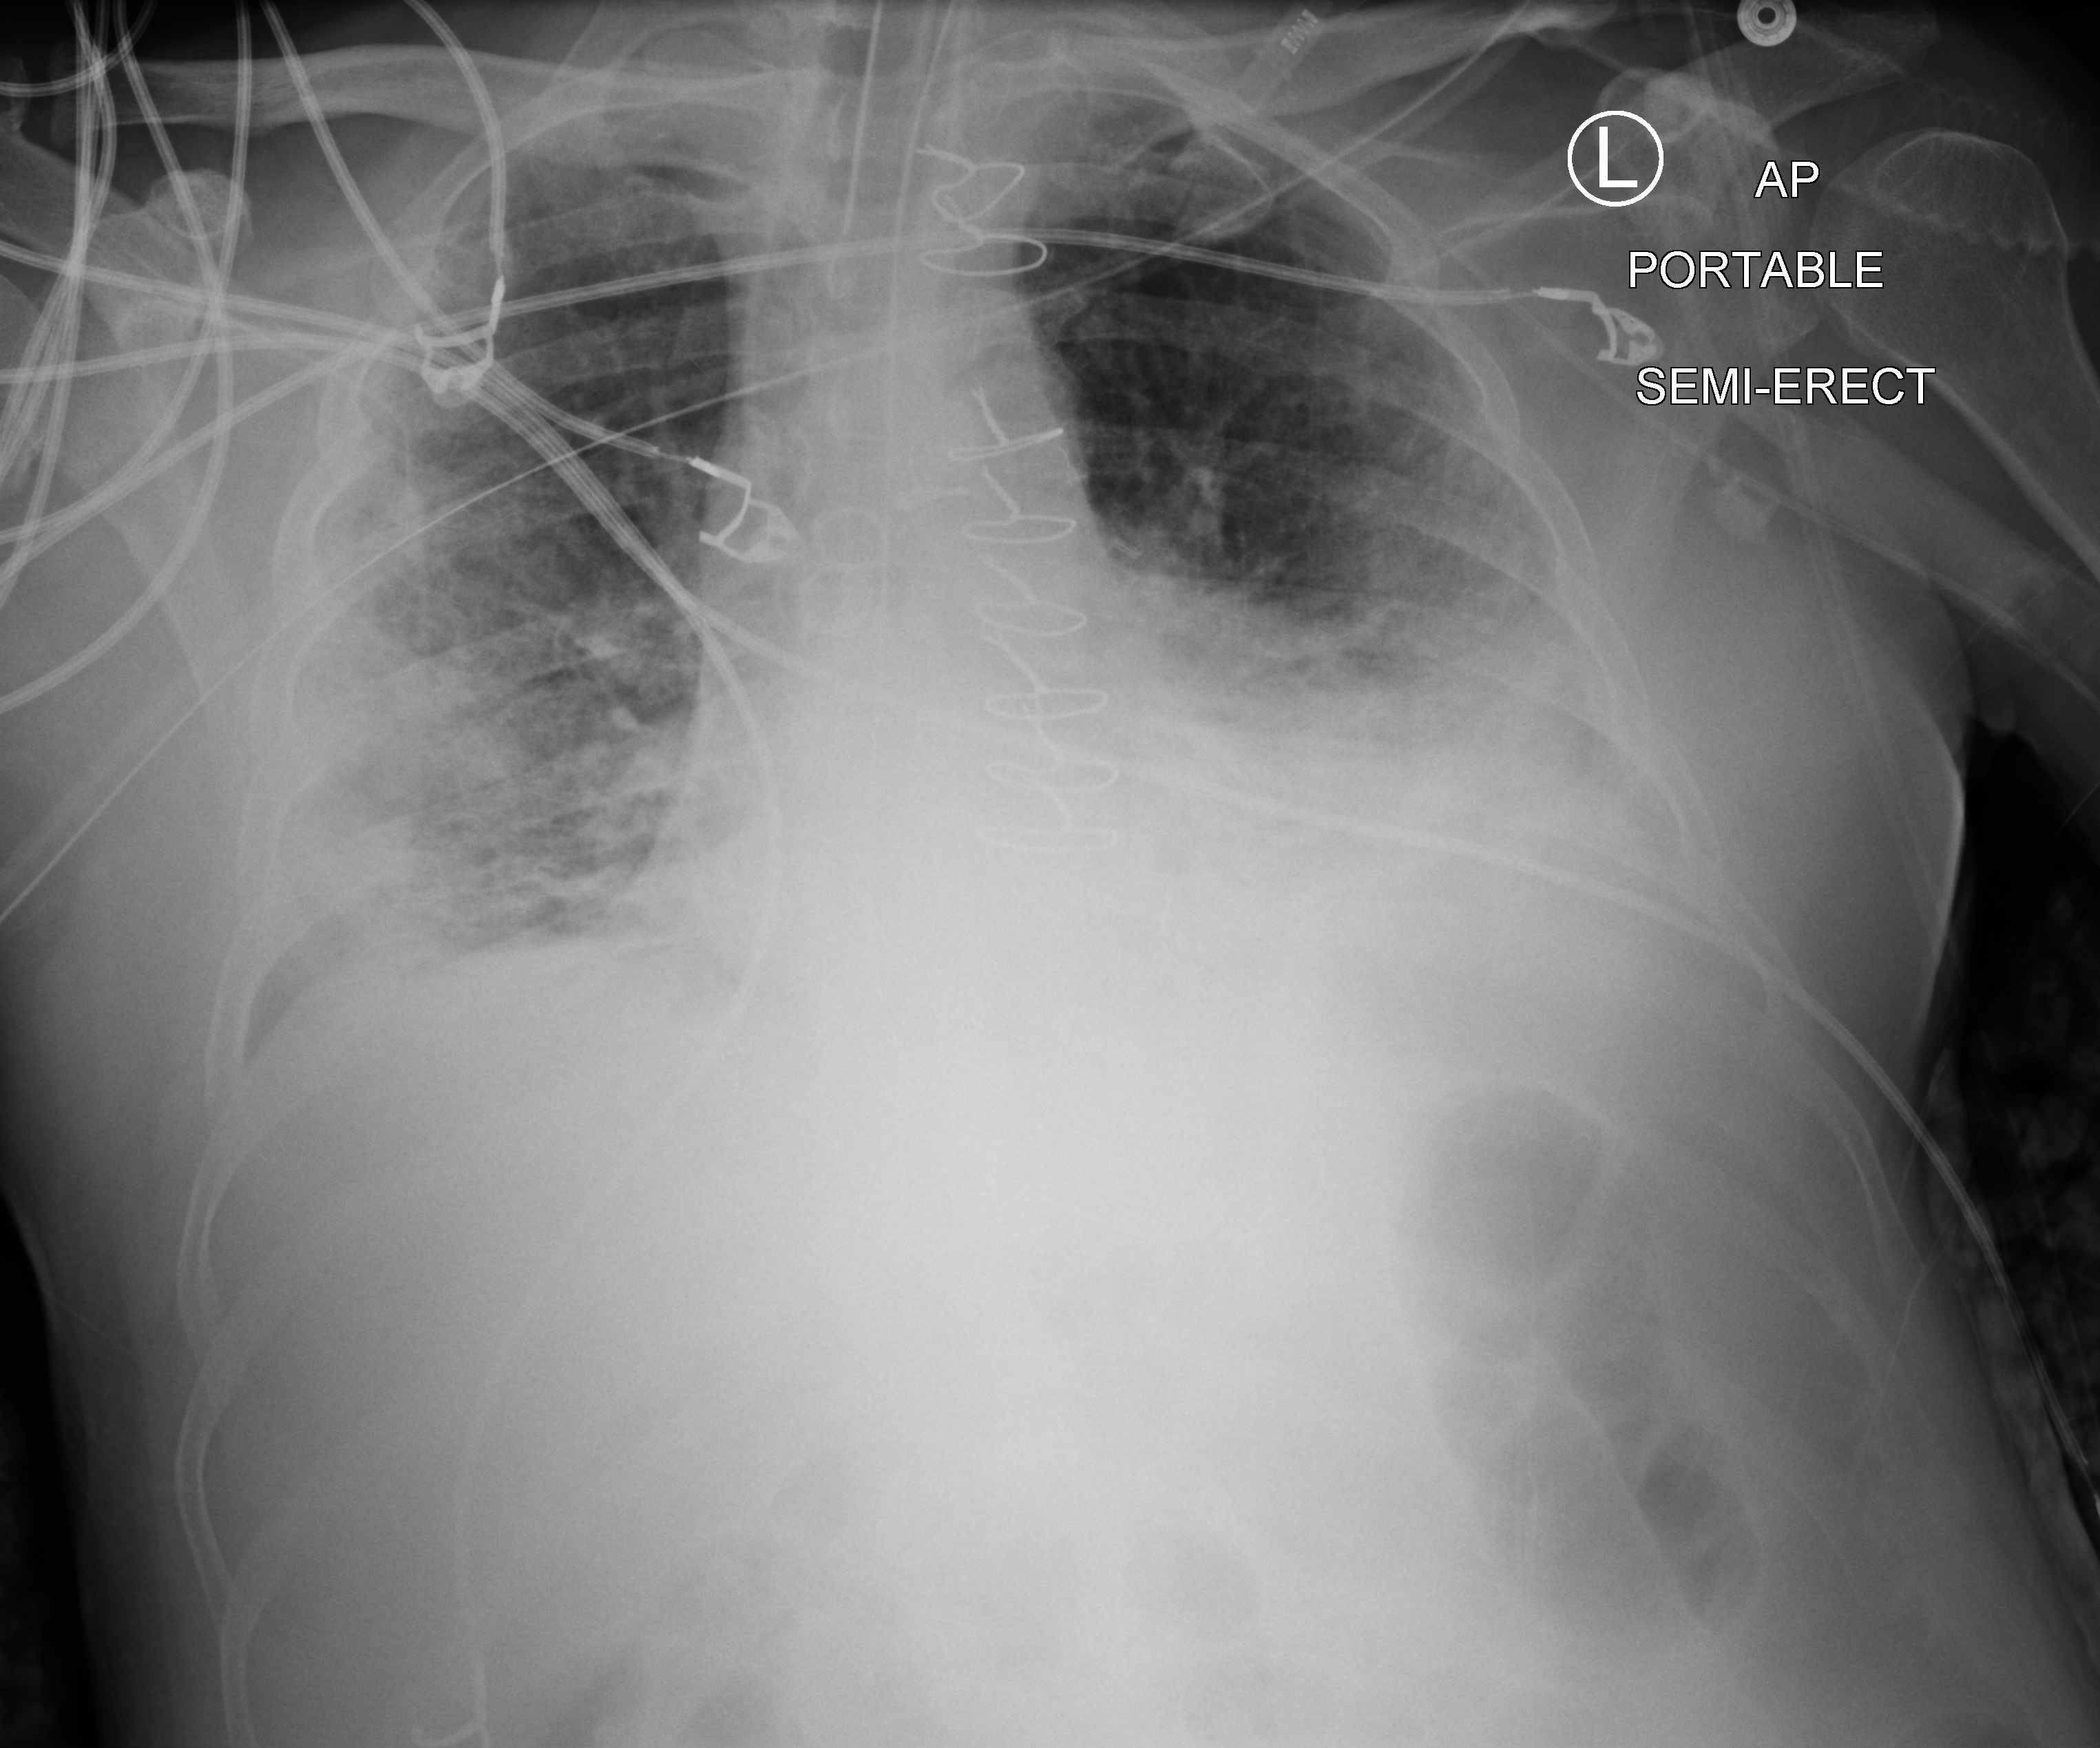
Portable chest radiograph, anteroposterior (AP) projection. Patient hospitalised with COVID-19; male, aged 18–59 years.
Hospital-stay facts (about this admission, not read from this image; timing relative to this image not recorded):
- length of hospital stay: 63 days
- smoking status (admission record): former
- diabetes (admission record): yes